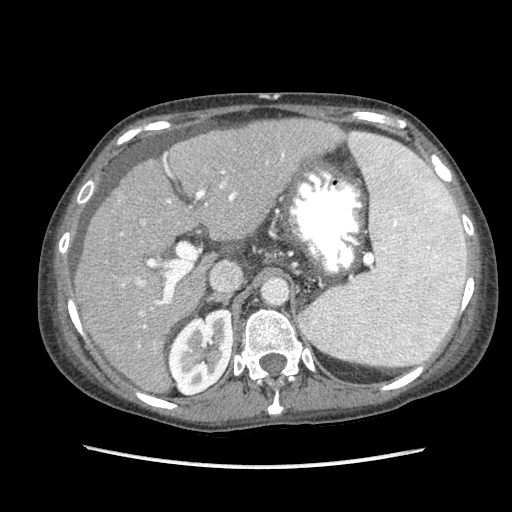
Contrast-enhanced abdominal CT (liver protocol), one axial slice; position 55 of 87 along the scan axis; soft-tissue window (W 400 / L 40 HU); 2.5 mm slice thickness; 512 × 512 image matrix, field of view 340 × 340 mm. Case-level facts recorded for this patient, not image findings: diagnosis: hepatocellular carcinoma (patient treated with transarterial chemoembolisation; whether this scan precedes or follows treatment is not stated here); TNM stage (as recorded): Stage-IIIB; Child-Pugh class: A; tumour differentiation: no biopsy; tumour nodularity: uninodular.
Structures marked on this image (semi-automatically segmented with operator editing):
- liver parenchyma outside the tumour (the mass and vessels are separate outlines, so this box may not span the whole liver): bounding box (x1, y1, x2, y2) in pixels: (74, 118, 389, 392)
- mass: (104, 200, 121, 214)
- liver vessels: (120, 132, 388, 347)